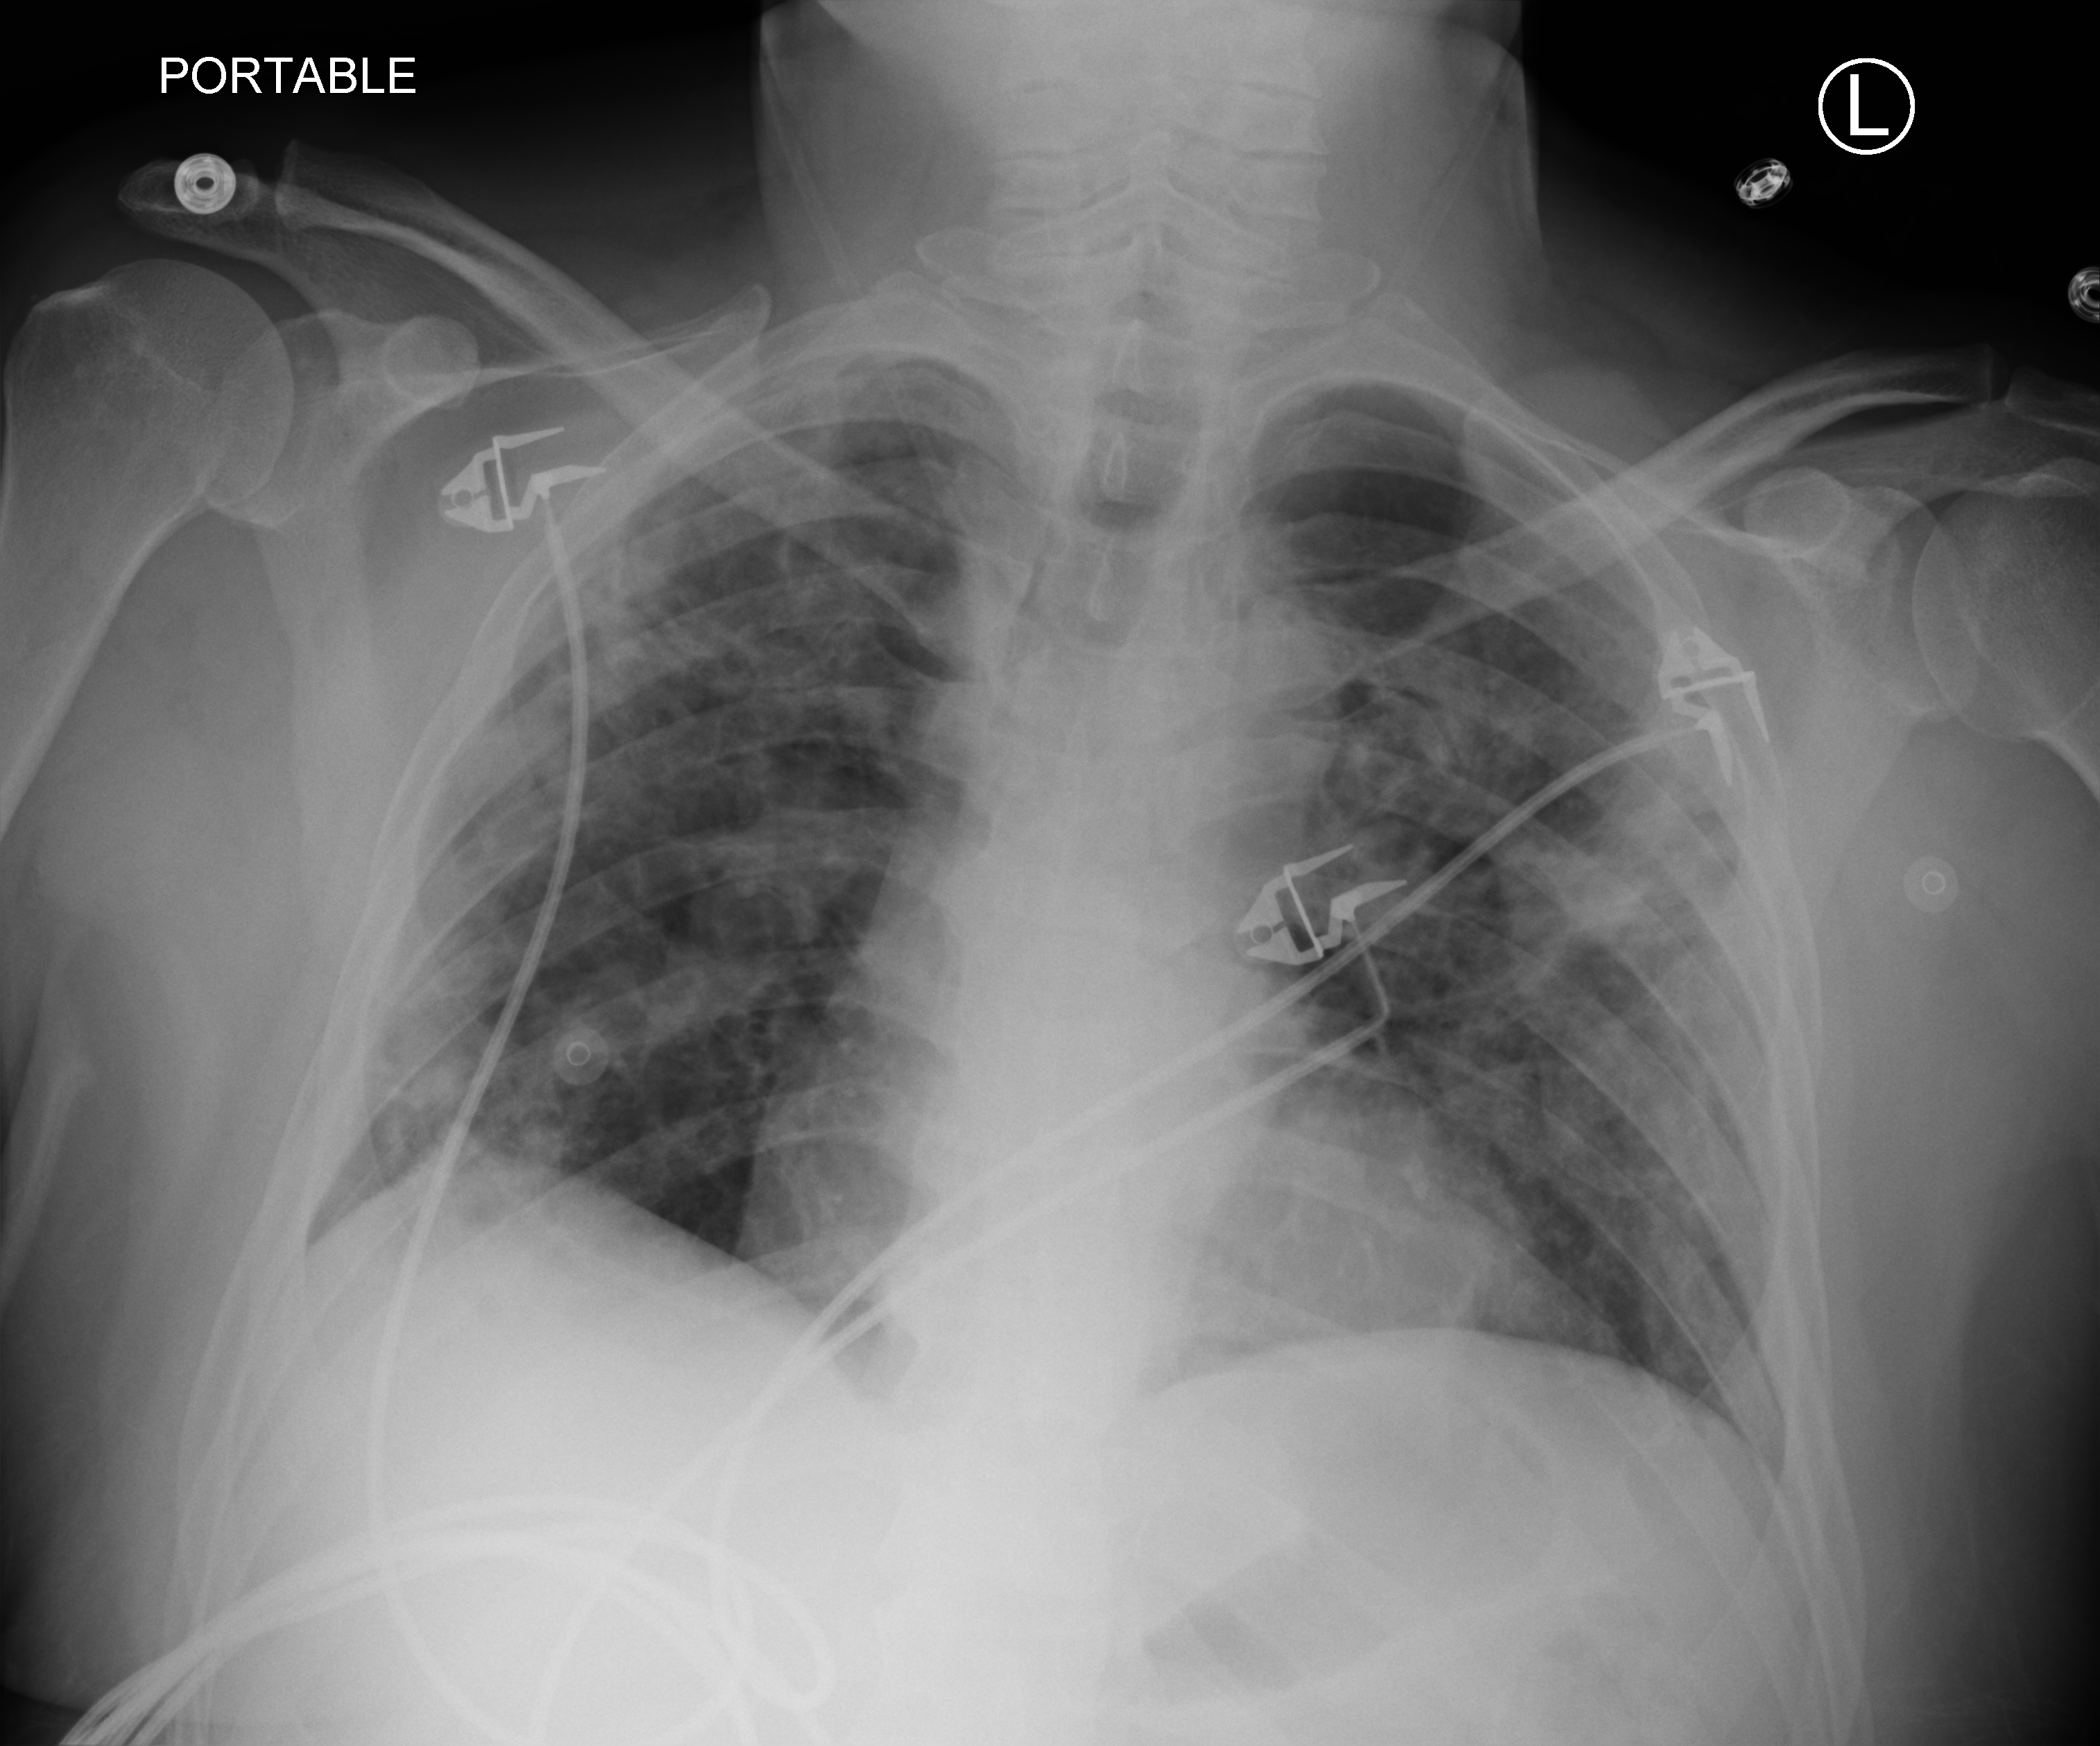
Portable chest radiograph; anteroposterior (AP) projection. Male patient hospitalised with COVID-19, age 18–59 years.
Admission-level facts for this patient (not findings on this image; timing relative to this image not recorded):
- mechanically ventilated during this hospital stay: no